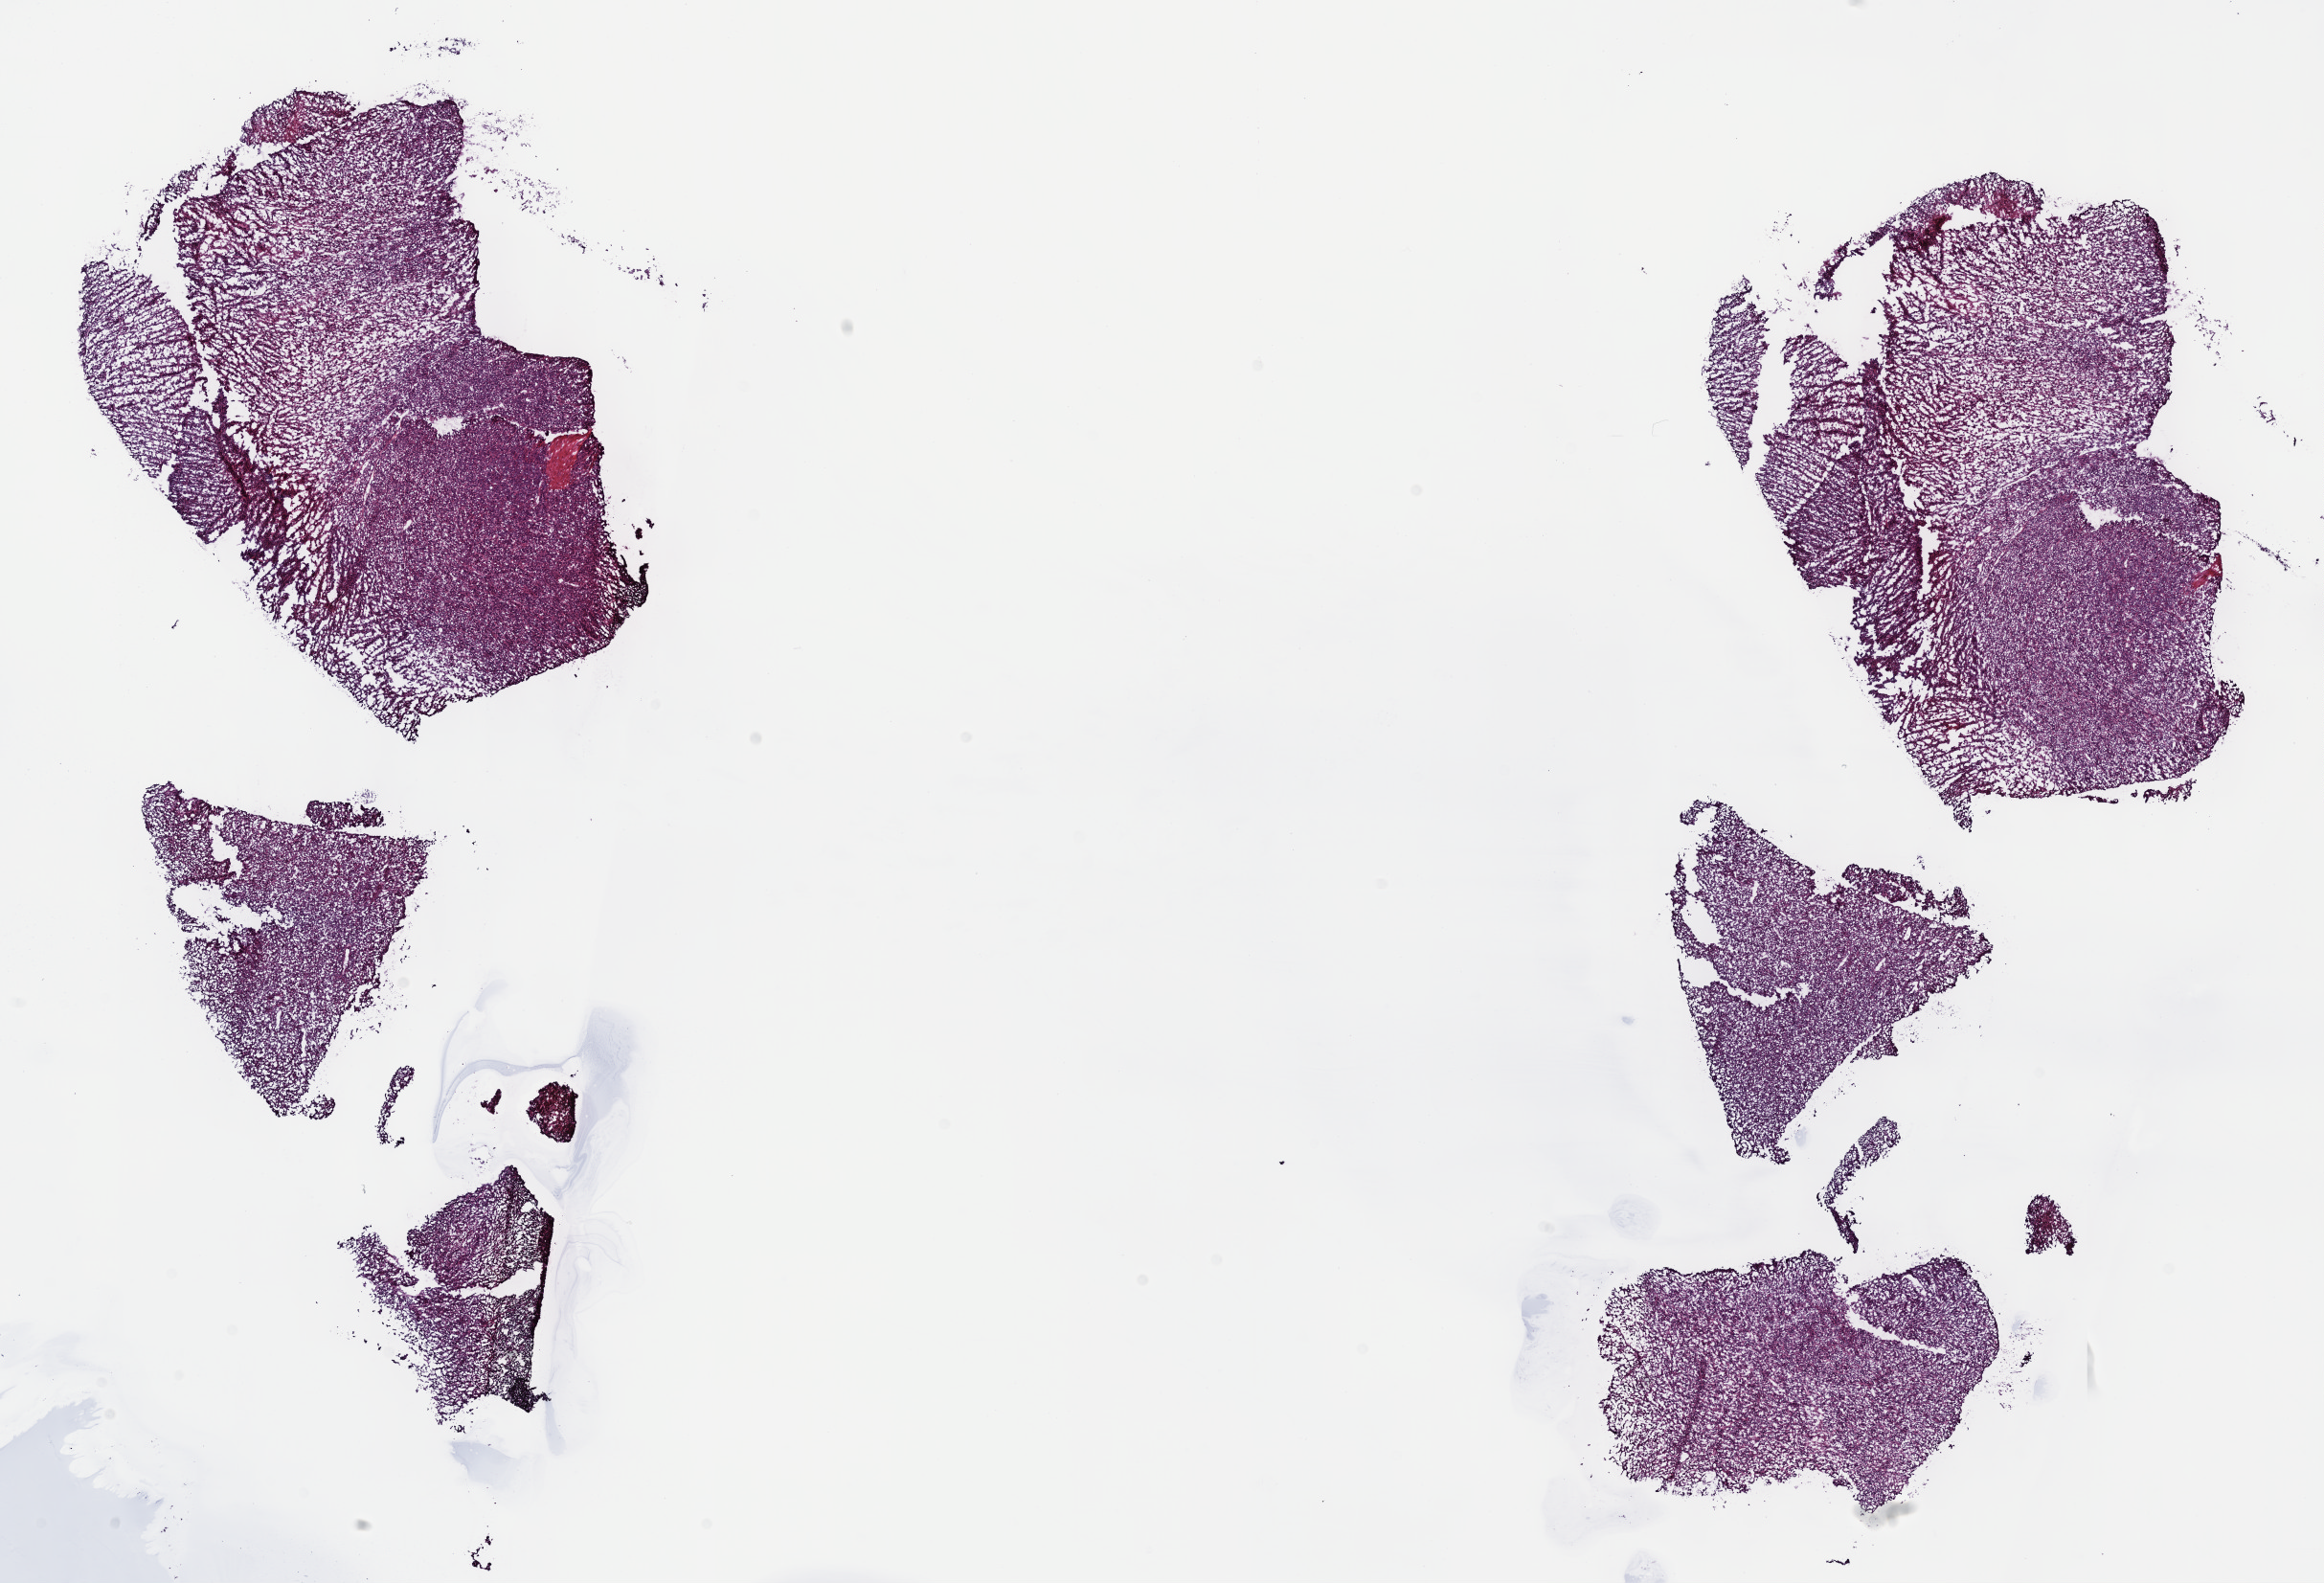
Digitized Hematoxylin and eosin (H&E) stained tissue section (whole slide) — whole scanned area (about 19.6 x 13.4 mm, acquisition: 40x scan) shown as a low-resolution overview. Frozen section. Primary tumour sample from the uterus. Female patient; age at initial diagnosis 48 years. Composition of this section per pathologist review: tumour cells 100%, tumour nuclei 80%, normal cells 0%, stromal cells 0%, necrosis 0%. Inflammatory infiltration, as recorded: lymphocyte infiltration 1%, monocyte infiltration 0%, neutrophil infiltration 0%.
• diagnosis: Leiomyosarcoma, NOS